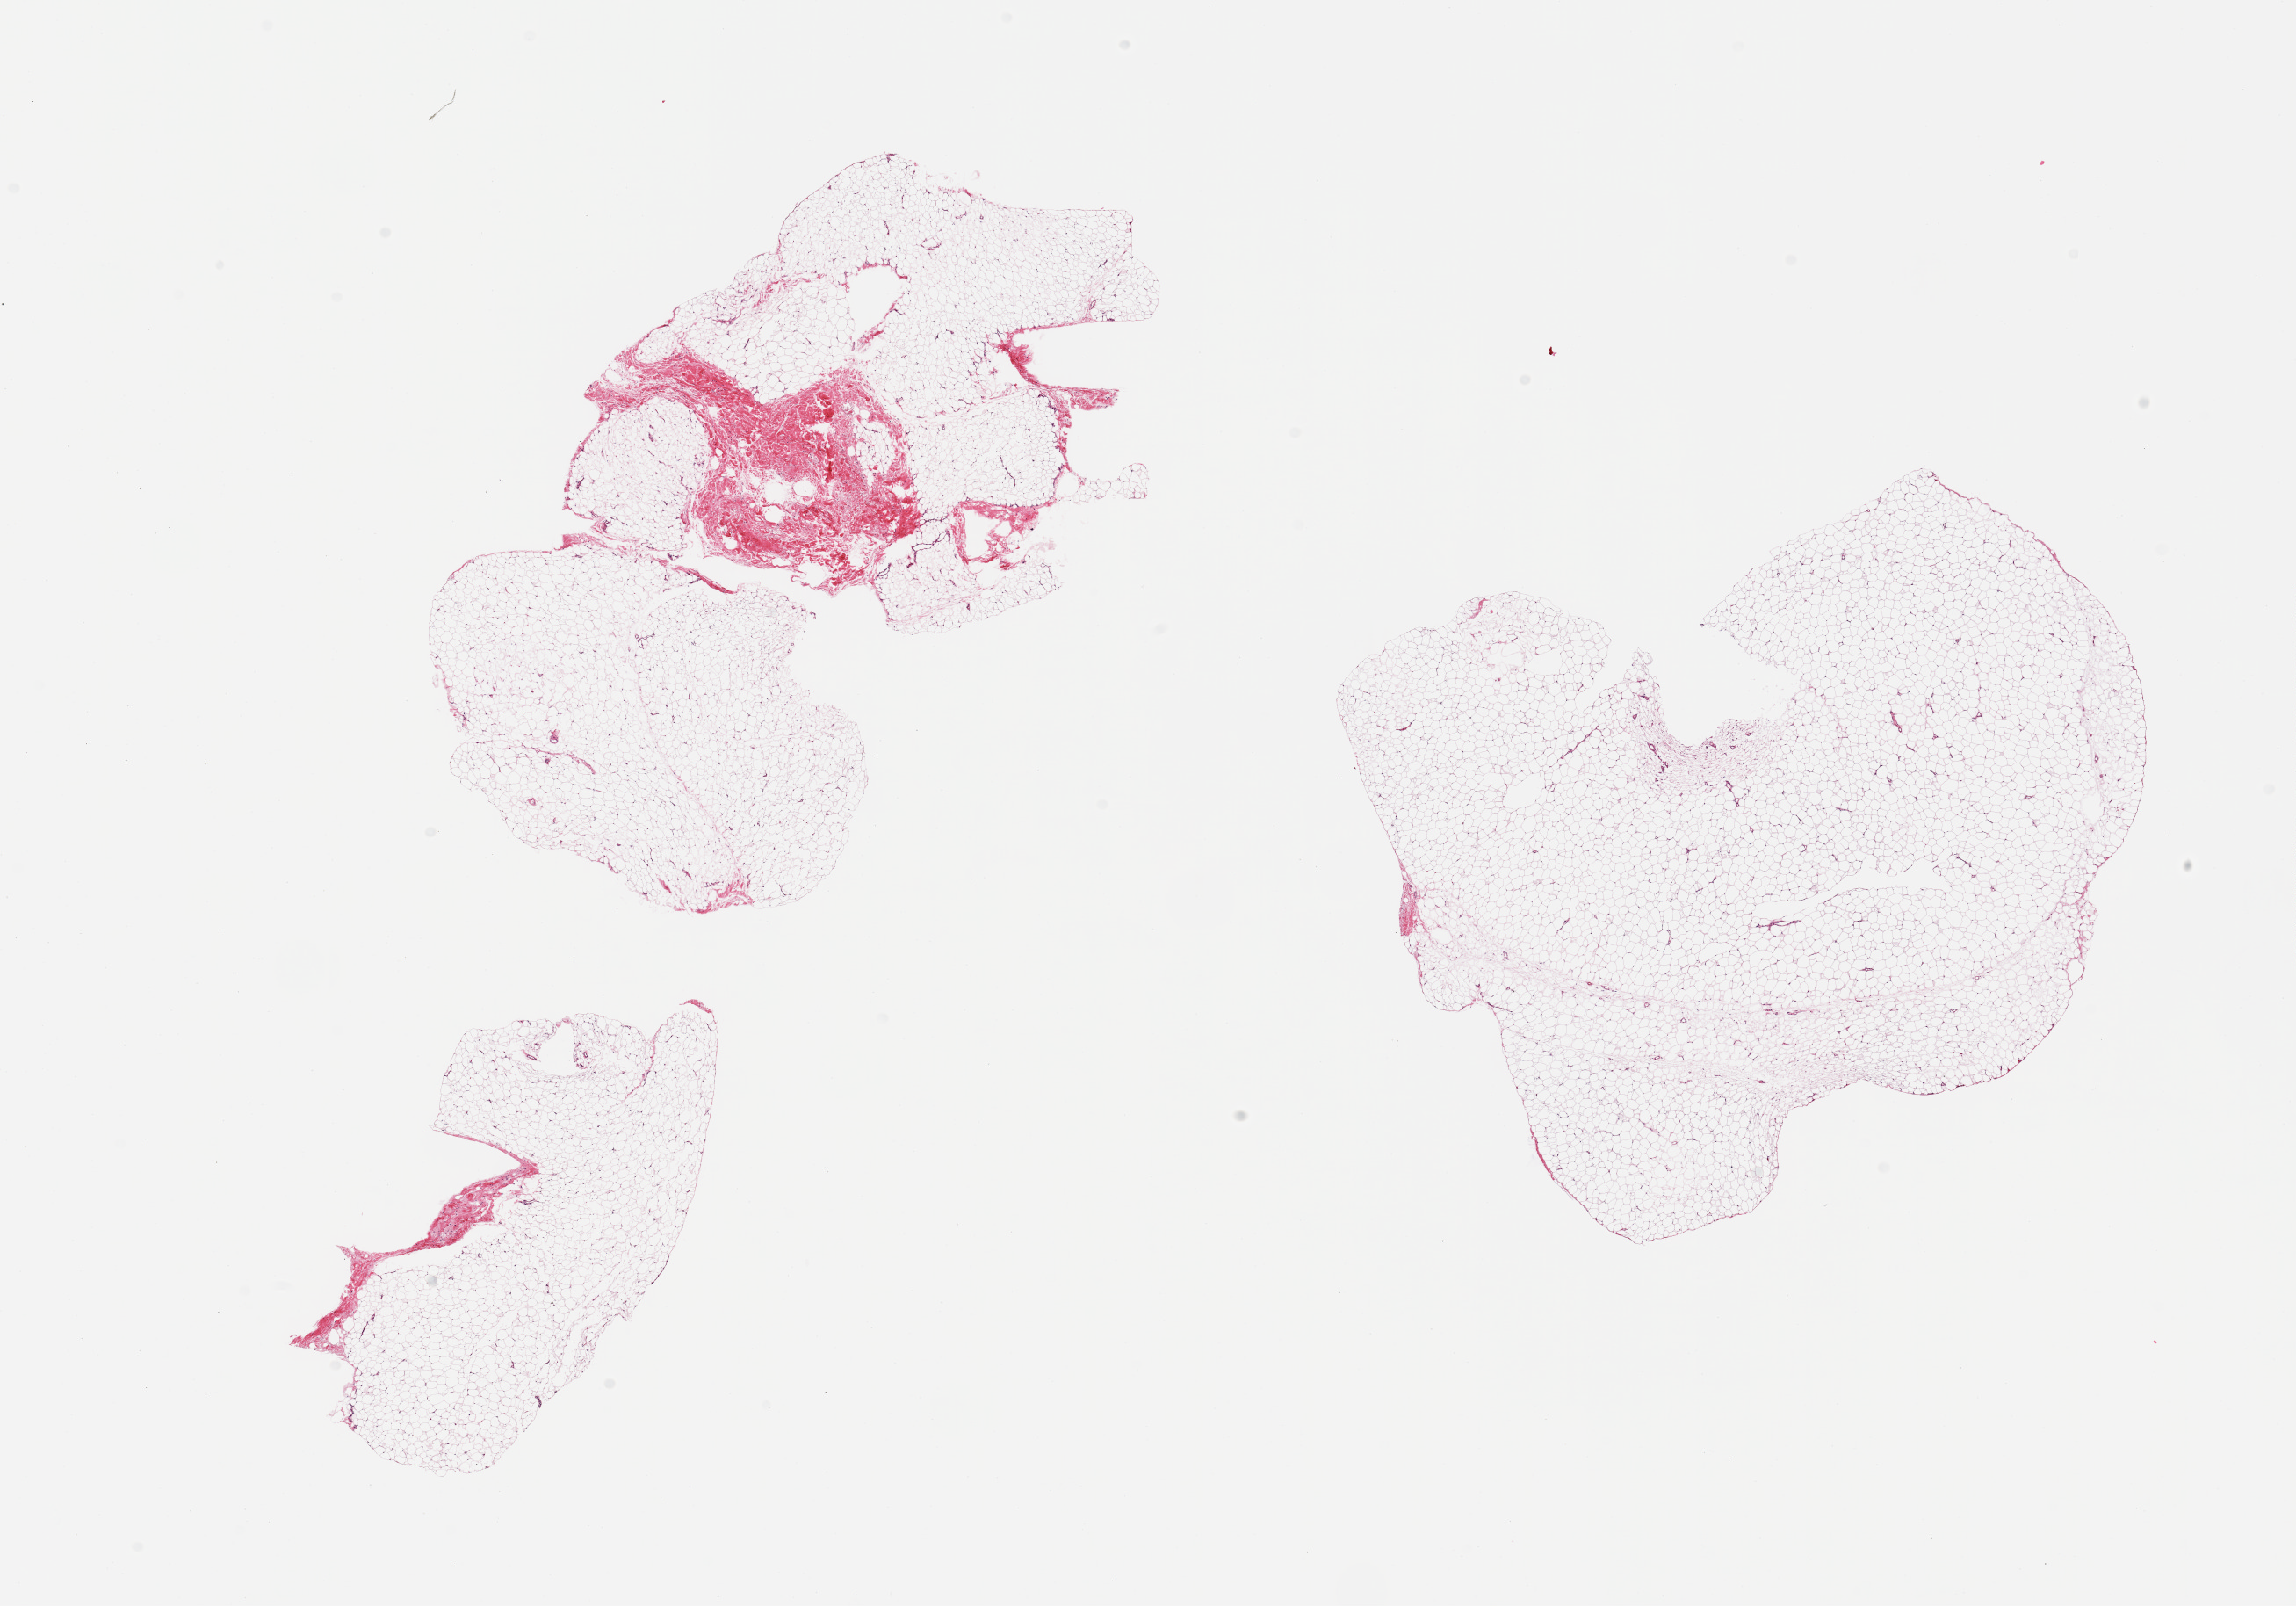
Haematoxylin and eosin whole-slide image, brightfield, a low-resolution overview of the entire scanned area, about 20.7 x 14.5 mm (slide scanned at 20x). PAXgene-fixed paraffin-embedded (PFPE) section. Sampled site (target tissue): adipose tissue. Donor tissue sample. Donor sex: male.
- review note (as recorded): 2 pieces, ~10% fascia